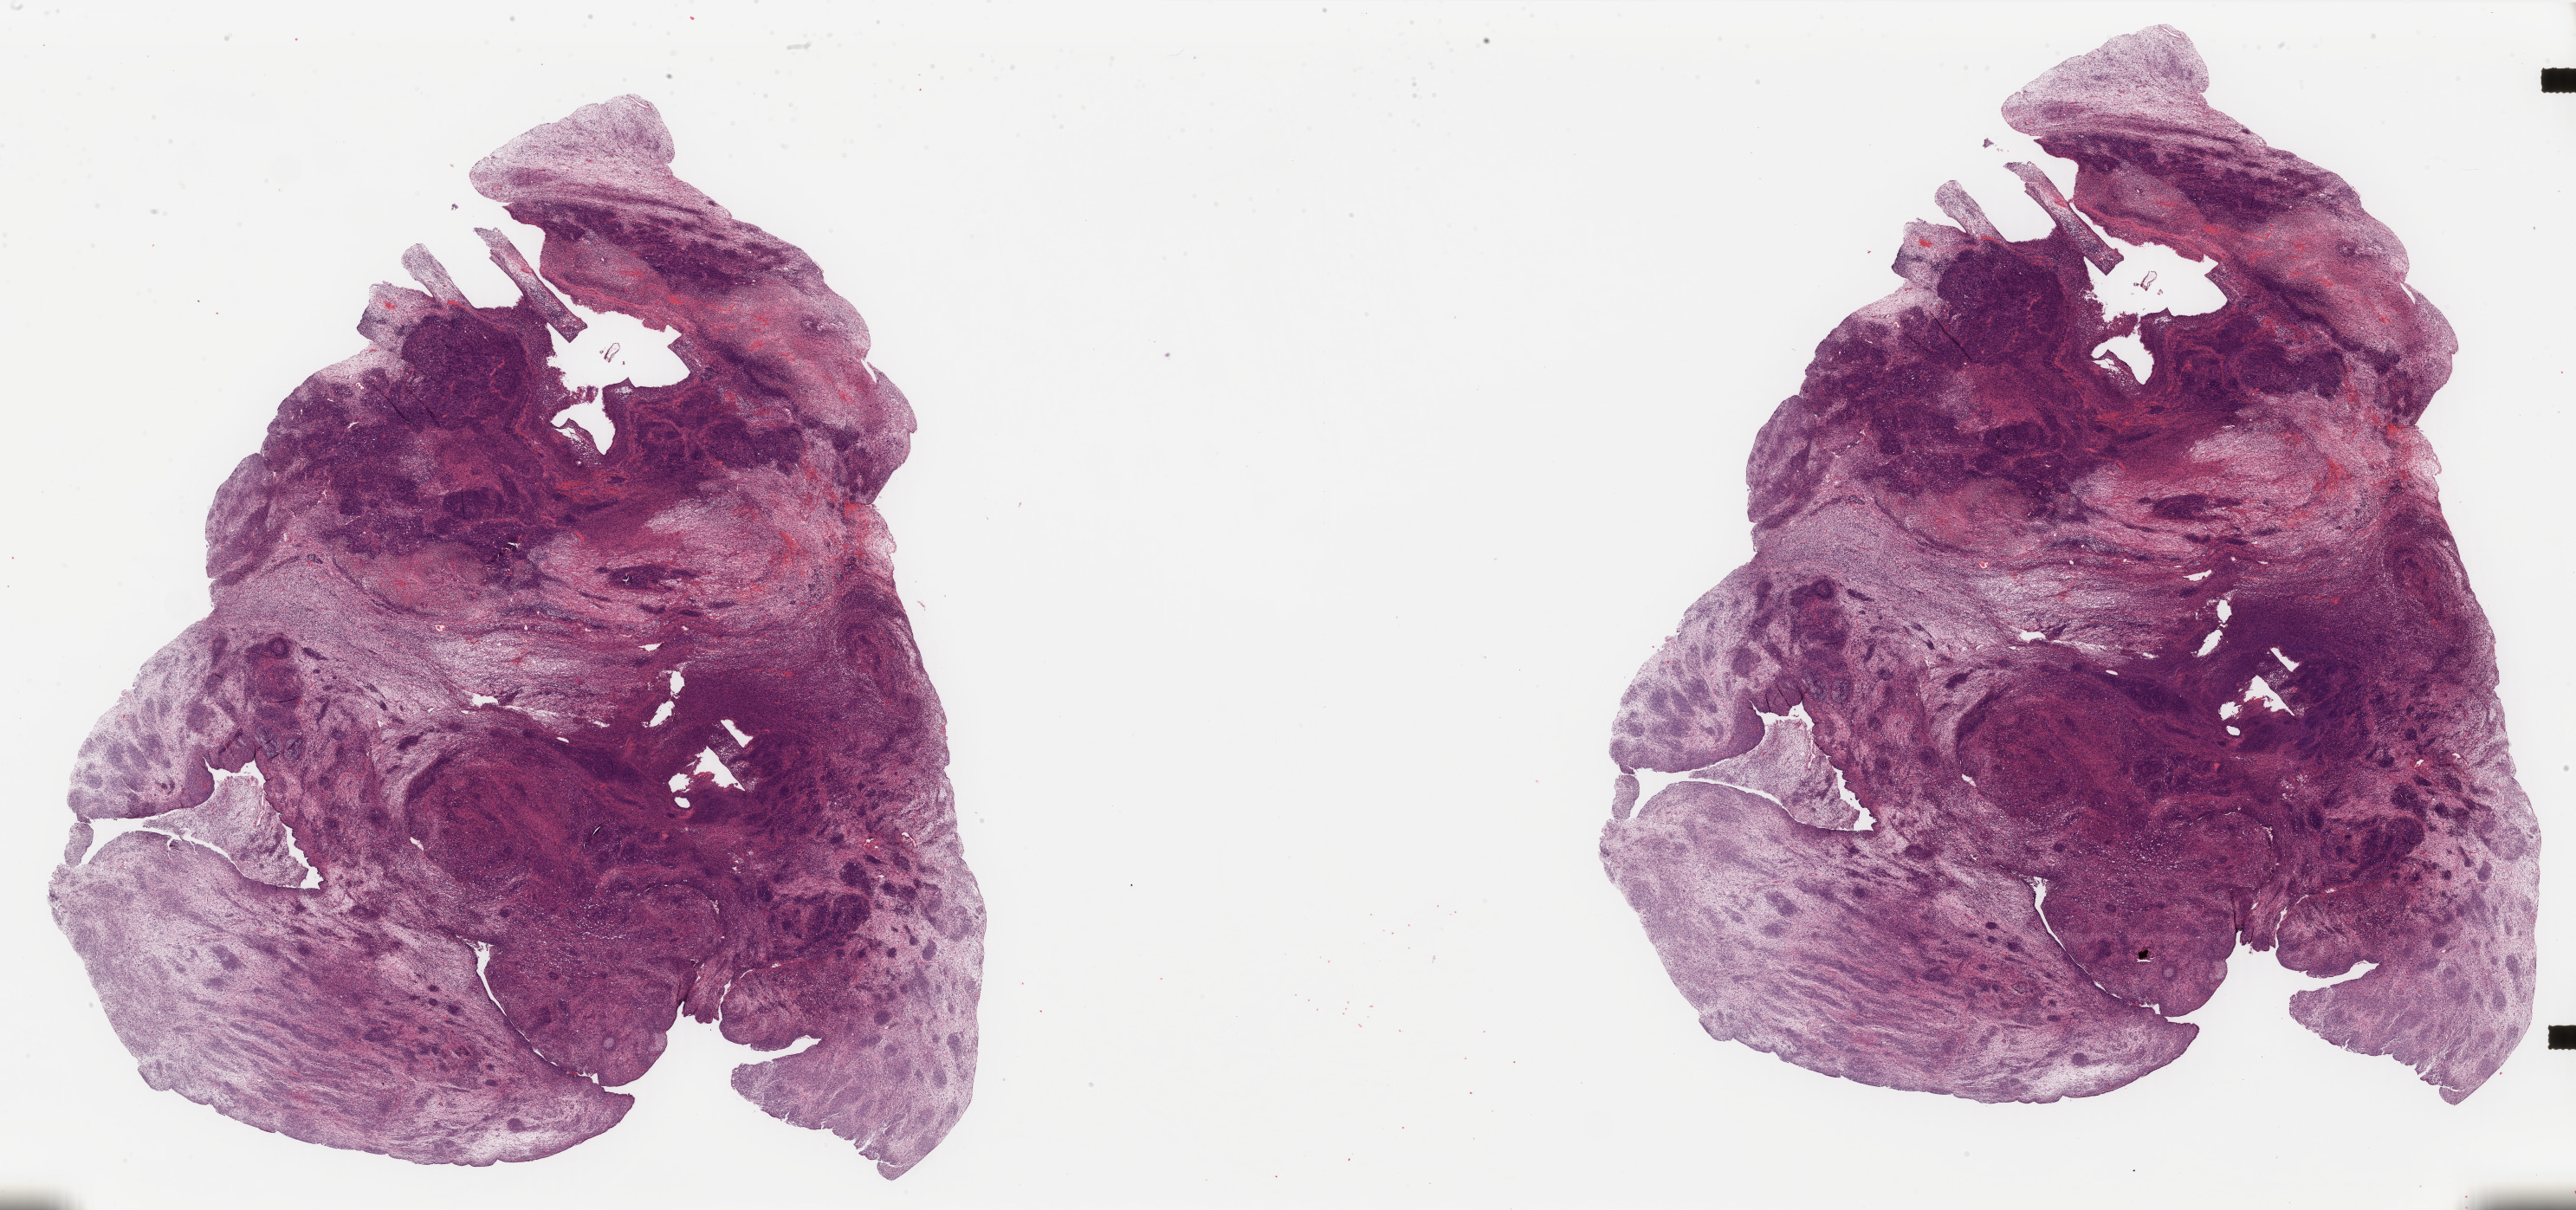
Digitized H&E-stained tissue section (whole slide) — a low-resolution overview of the entire scanned area, about 47.1 x 22.1 mm; formalin-fixed paraffin-embedded (FFPE) diagnostic section; primary tumour sample from the uterus. Female patient; age at initial diagnosis 68 years.
* lymph nodes positive (case pathology): 3 of 20 examined
* FIGO stage: IIIC1
* pathologic diagnosis: Carcinosarcoma, NOS (endometrium)